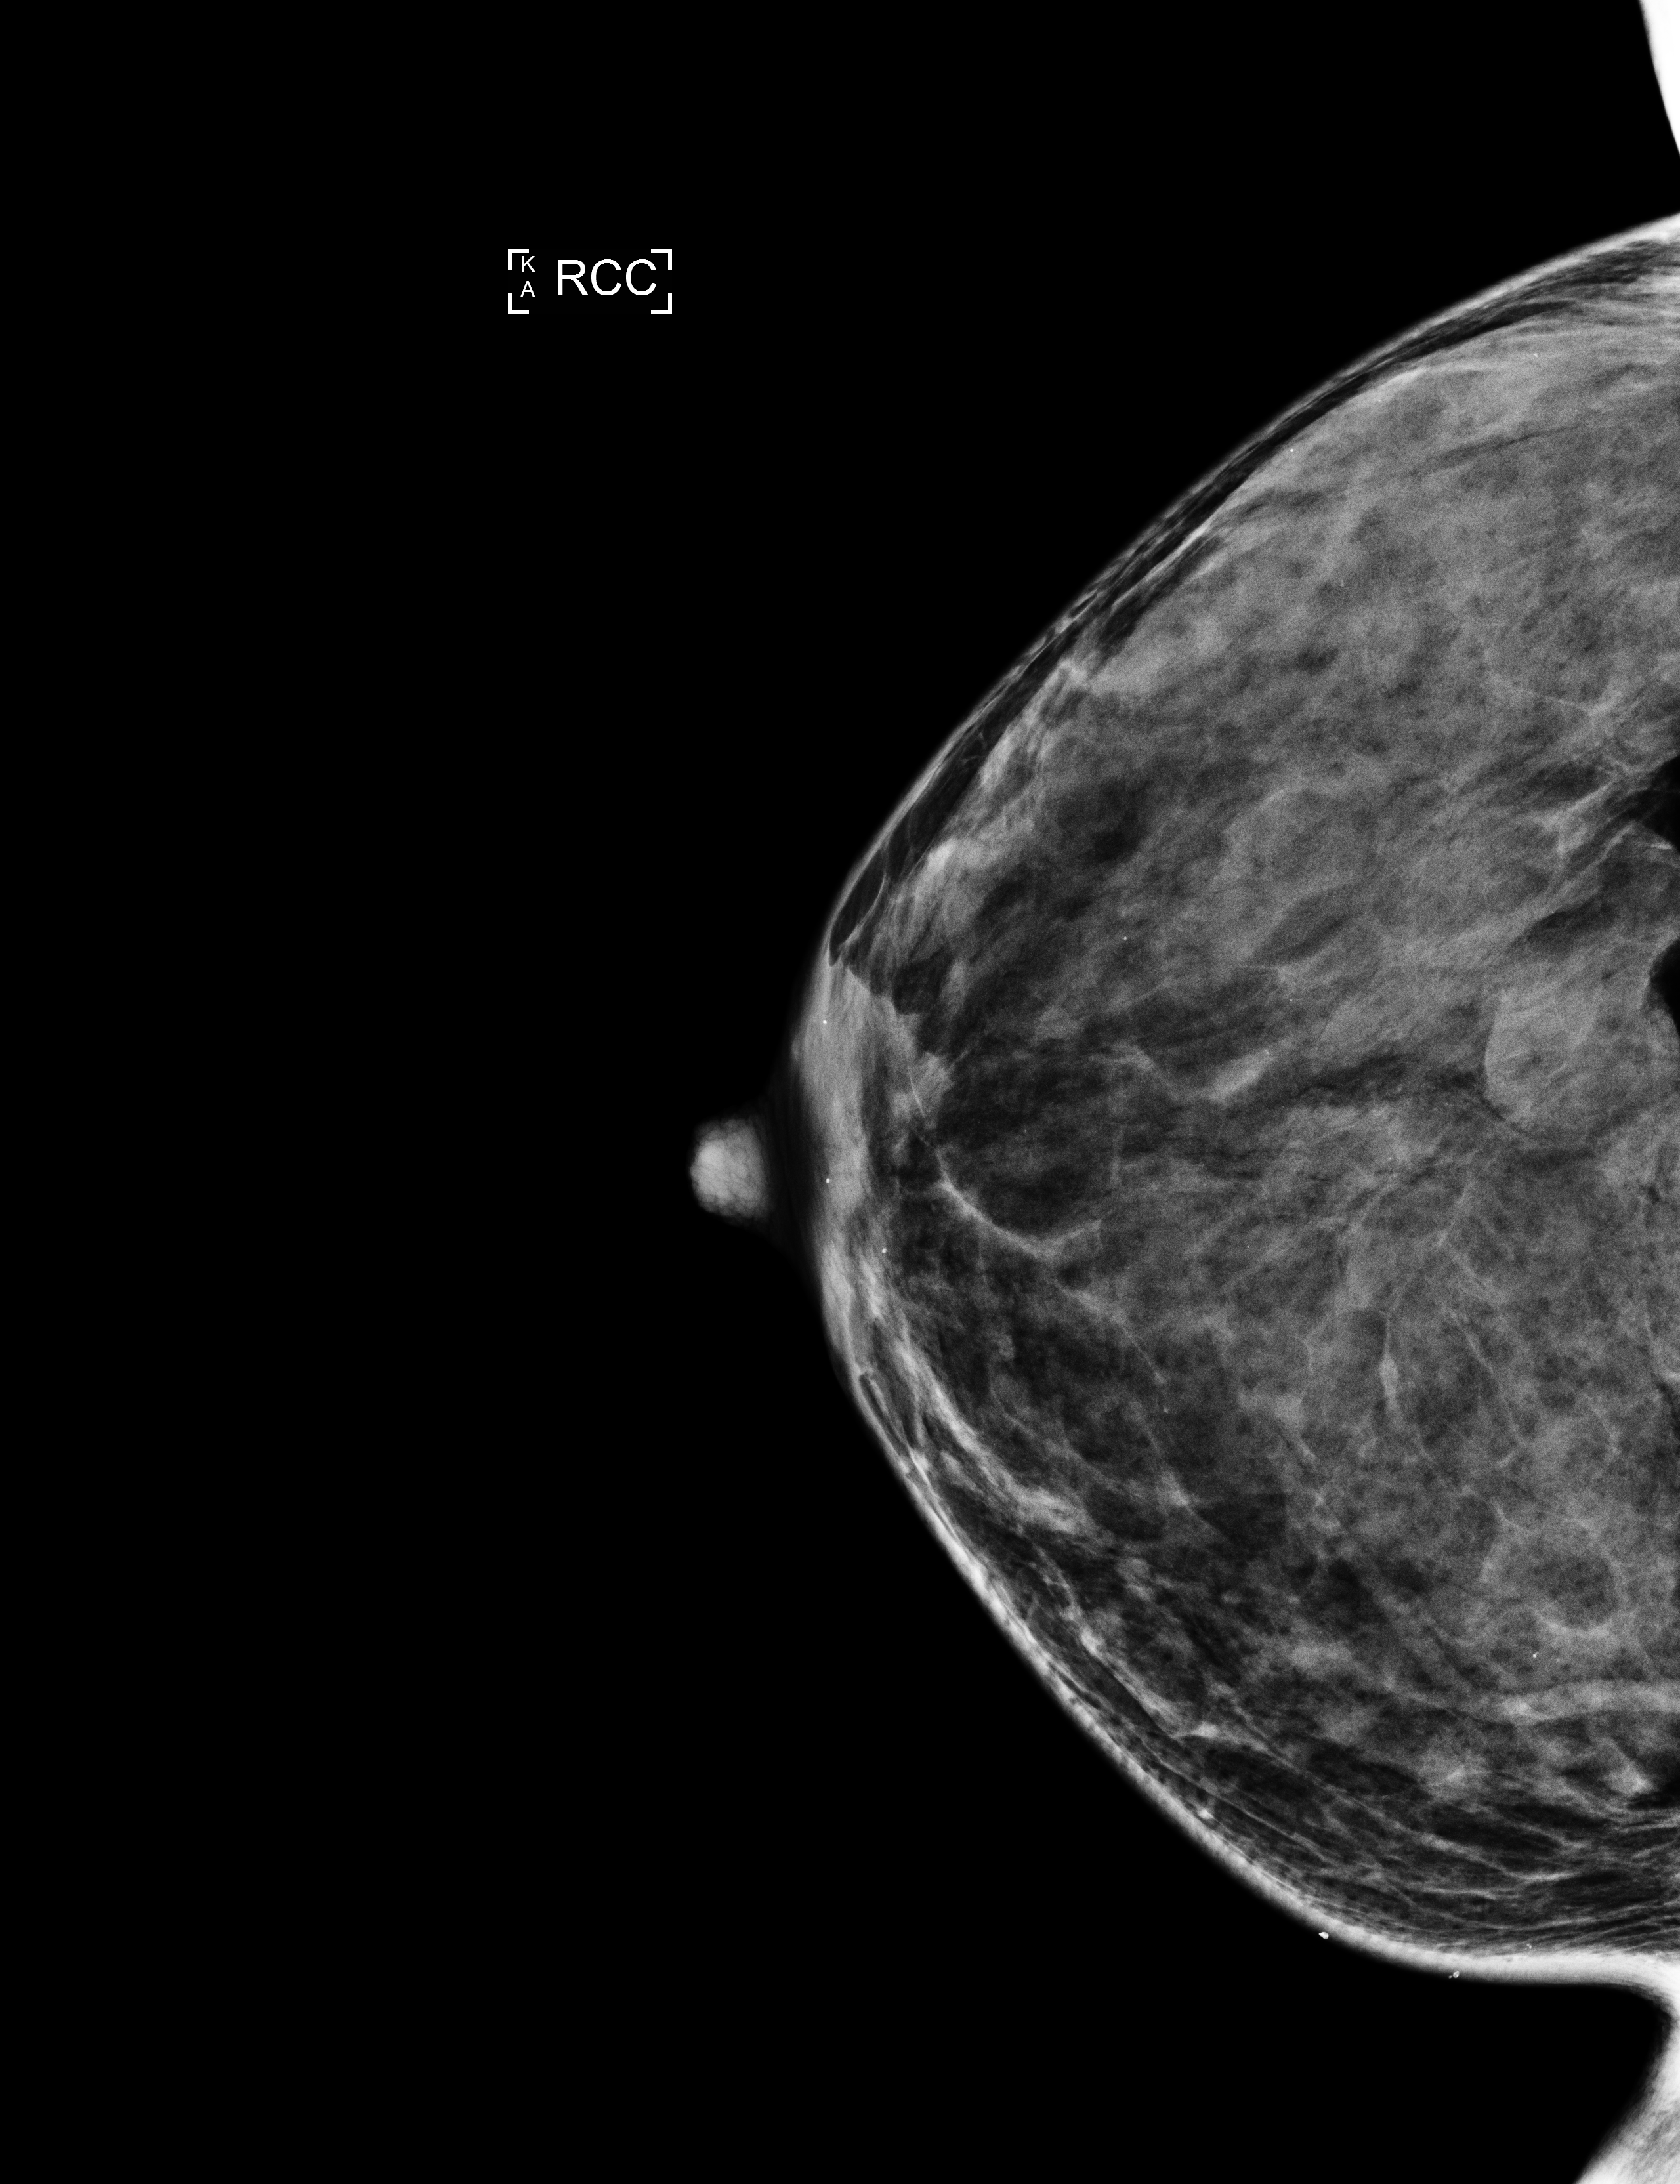
Digital mammogram (FFDM); right breast; CC view; screening examination. Patient: female, 41 years.
Breast density at the screening exam (both breasts): extremely dense (BI-RADS density category d). Final BI-RADS category for the screening round (tomosynthesis exam, both breasts): category 2. Recall: no recall after this screen.